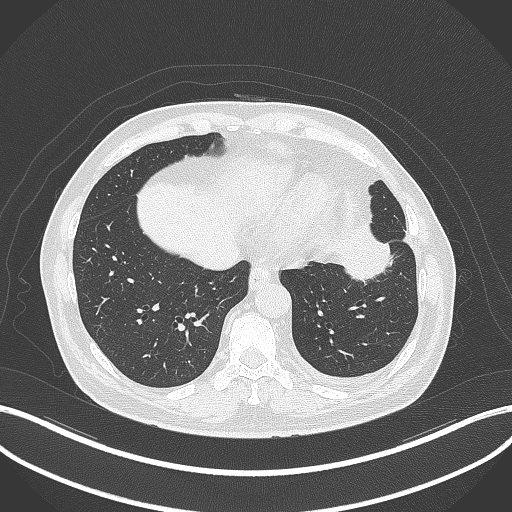
Chest CT, one axial slice; position 95 of 230 along the scan axis; 120 kVp; lung window (W 1500 / L -600 HU); 1 mm slice thickness; 512 × 512 image matrix, field of view 400 × 400 mm. Male patient, age 68 years. Case-level facts recorded for this patient, not image findings: clinical TNM (as recorded): T2b N0 M0.
Annotated regions visible in this slice (bounding box drawn by a radiologist):
- lung tumour (recorded histology: squamous cell carcinoma): box from (x=335, y=225) to (x=397, y=289) px